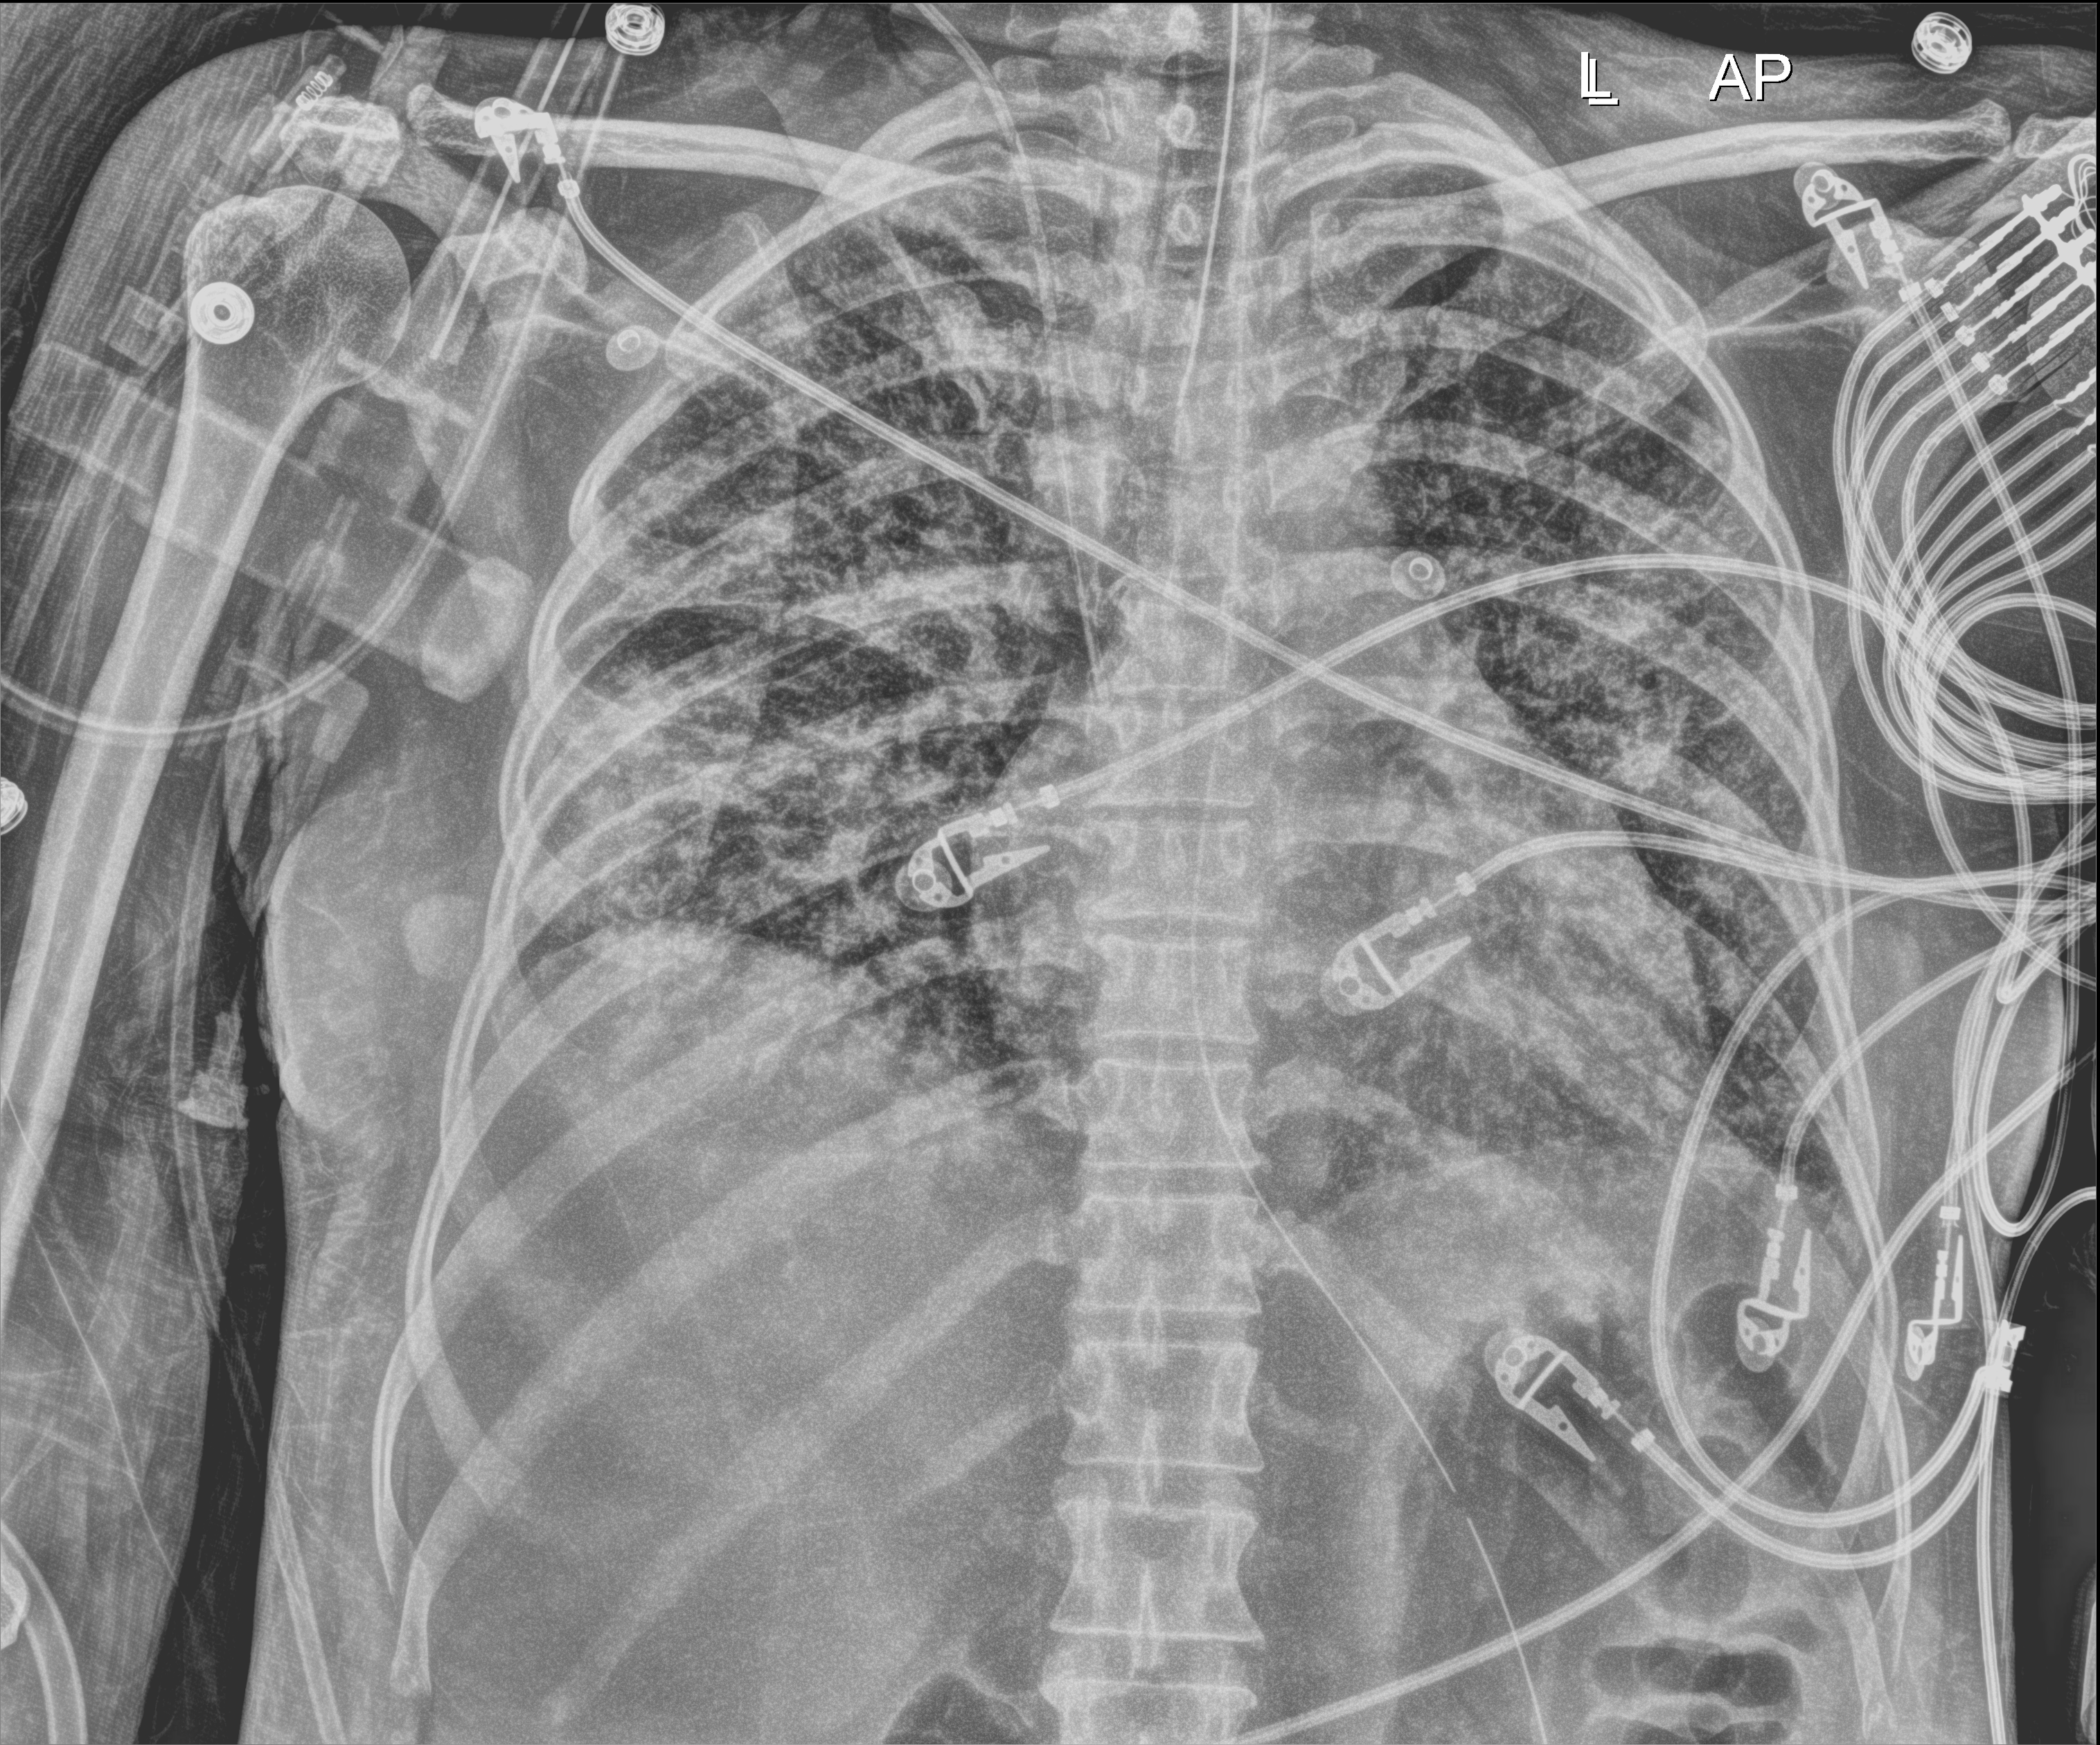
Chest X-ray (portable). Patient hospitalised with COVID-19; female, aged 18–59 years.
Admission-level facts for this patient (not findings on this image; timing relative to this image not recorded):
- mechanically ventilated during this hospital stay: yes
- length of hospital stay: 71 days